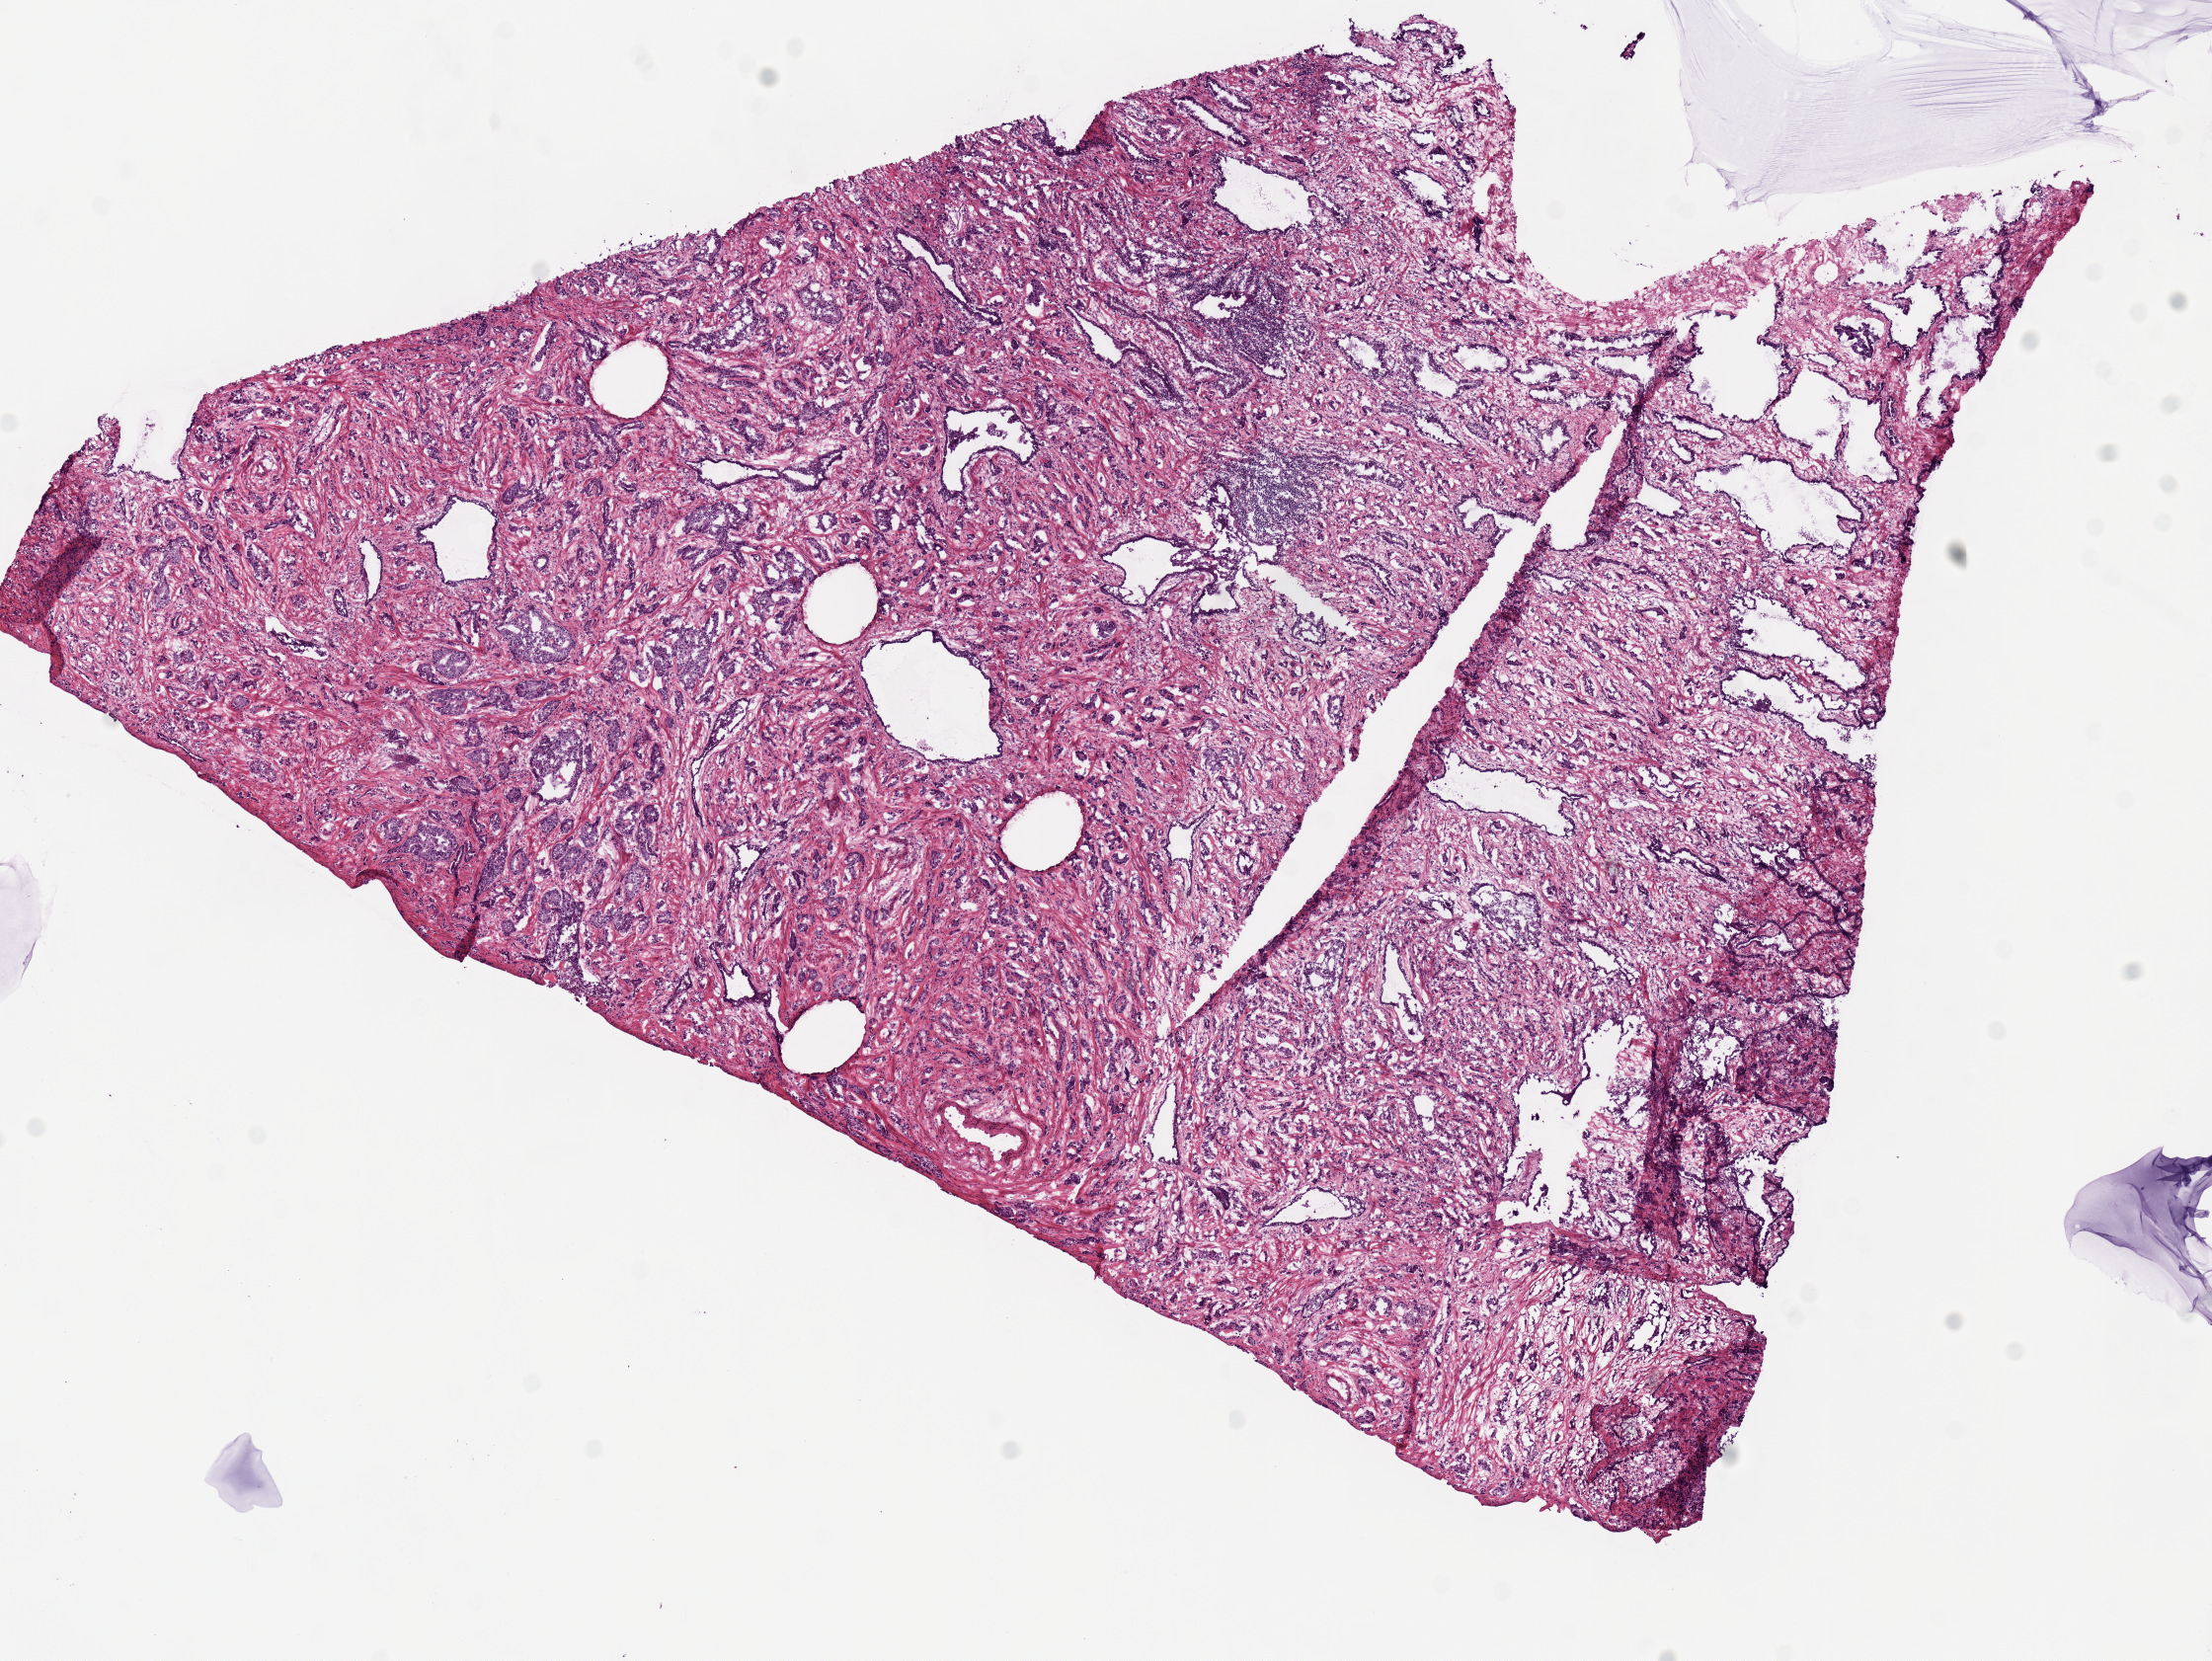
Hematoxylin and eosin (H&E) stained whole-slide image, whole scanned area (about 8.9 x 6.6 mm, slide scanned at 20x) shown as a low-resolution overview; frozen section; sample: primary tumour, prostate. Male, age 70 years at initial diagnosis. Gleason score: 7 (4+3). Pathologist review of this section (percent, as recorded): tumour nuclei 70%, necrosis 0%.
• diagnosis: Acinar cell carcinoma
• lymph nodes positive (case pathology): 0 of 9 examined